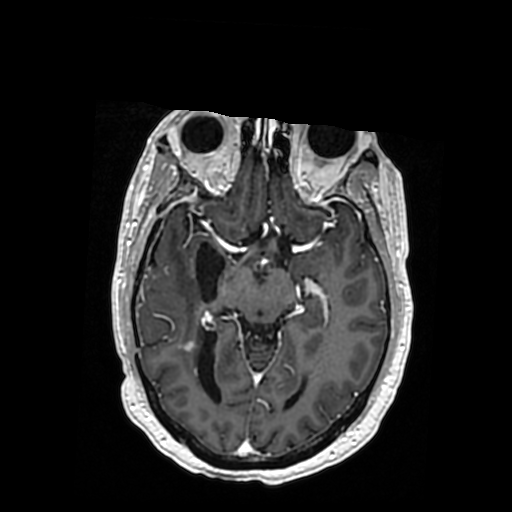
Brain MRI from a brain-tumour surgery series, one axial slice. Slice 205 of 364 in the series (ordered by position). T1-weighted post-contrast. 512 × 512 image matrix, field of view 260 × 260 mm. Case-level facts recorded for this patient, not image findings: histopathology: Oligodendroglioma; WHO grade: 3; IDH mutation: yes.
Annotated regions visible in this slice (expert manual segmentation):
- previous resection cavity: bounding box <150,242,225,301> (left, top, right, bottom; pixels)
- tumour: <167,337,175,346>